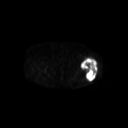
FDG PET of an extremity soft-tissue mass (from a PET/CT study), one axial slice. Slice 239 of 267 in the series (ordered by position). 3.27 mm slice thickness. 128 × 128 image matrix, field of view 700 × 700 mm. Patient: female, 62 years. Case-level facts recorded for this patient, not image findings: histological type: undifferentiated – high grade; grade: high; site of the primary tumour: left thigh.
Structures marked on this image (expert contour drawn on MRI and transferred to this co-registered scan by the dataset authors):
- gross tumour volume including surrounding oedema: bounding box <81,58,98,81> (left, top, right, bottom; pixels)
- gross tumour volume (mass): <81,58,98,81>